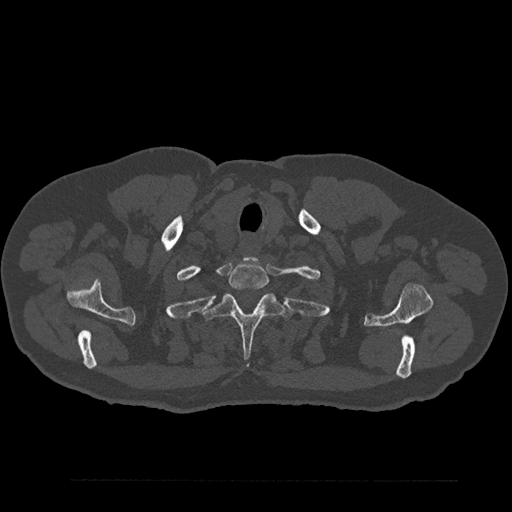
CT including the spine, one axial slice; slice 730 of 797 in the series (ordered by position); reconstruction kernel Br40s/3; bone window (W 1800 / L 400 HU); 0.5 mm slice thickness; 512 × 512 image matrix, field of view 430 × 430 mm. Patient: male, 61 years. Case-level facts recorded for this patient, not image findings: primary cancer: prostate.
Outlined on this slice (semi-automatically segmented with operator editing):
- T1 vertebra: box from (x=228, y=262) to (x=269, y=290) px
- T2 vertebra: (x=206, y=294)–(x=291, y=357)